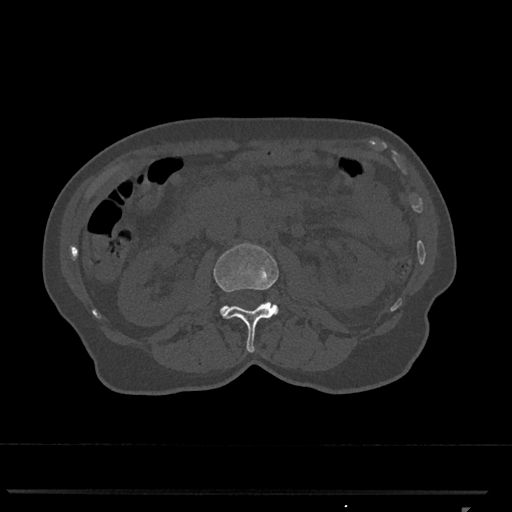
CT including the spine, one axial slice; slice 327 of 793 in the series (ordered by position); reconstruction kernel Br40s/3; 120 kVp; bone window (W 1800 / L 400 HU); 512 × 512 image matrix, field of view 380 × 380 mm. Patient: female, 62 years. Case-level facts recorded for this patient, not image findings: primary cancer: renal.
Outlined on this slice (semi-automatic segmentation, software-assisted and operator-edited):
- L2 vertebra: bounding box [x1, y1, x2, y2] px = [214, 243, 279, 353]